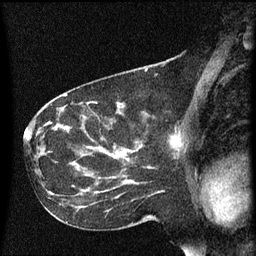
Breast MRI (dynamic contrast-enhanced), one sagittal slice; slice 32 of 60 in the series (ordered by position); dynamic contrast-enhanced series, image 2 of 3 at this slice position (ordered by acquisition); 1.5 T; TE 4.2 ms, TR 8.4 ms; 2 mm slice thickness; 256 × 256 image matrix, field of view 200 × 200 mm. Female patient, age 41 years. Case-level facts recorded for this patient, not image findings: setting: breast cancer imaged before/during neoadjuvant chemotherapy; receptor status: triple-negative.
Annotated regions visible in this slice (semi-automatically segmented with operator editing):
- analysis volume of interest (the breast-tissue region the enhancement analysis was run in; not a lesion): box from (x=138, y=112) to (x=181, y=157) px
- tumour enhancement mask (voxels above the 70 % enhancement threshold inside the analysis volume of interest): (x=174, y=140)–(x=176, y=143)